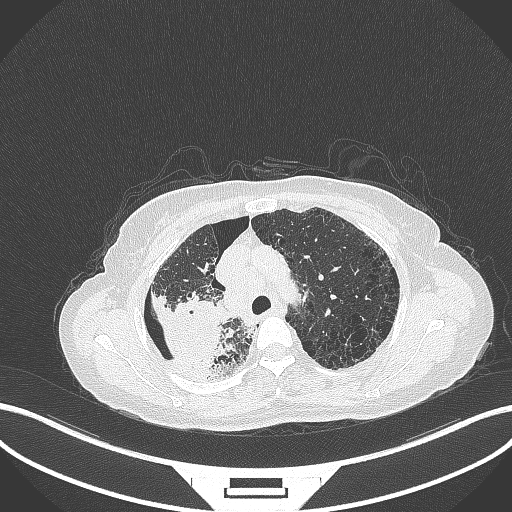
Chest CT, one axial slice; slice 264 of 408 in the series (ordered by position); reconstruction kernel B70f; lung window (W 1500 / L -600 HU); 1 mm slice thickness; 512 × 512 image matrix. Female patient, age 64 years. Case-level facts recorded for this patient, not image findings: clinical TNM (as recorded): T3 N3 M0.
Structures marked on this image (rectangle marked by the reading radiologist):
- lung tumour (recorded histology: squamous cell carcinoma): bounding box [x1, y1, x2, y2] px = [150, 286, 228, 375]